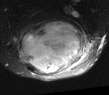
MRI of an extremity soft-tissue mass, one axial slice. Position 25 of 52 along the scan axis. T2-weighted fat-saturated. MR volume resampled by the dataset authors to the PET/CT grid (not the native acquisition matrix). 109 × 95 image matrix, field of view 106 × 93 mm. Male patient. Case-level facts recorded for this patient, not image findings: histological type: synovial sarcoma; site of the primary tumour: left poplietal fossa.
Outlined on this slice (expert contour drawn on MRI and transferred to this co-registered scan by the dataset authors):
- gross tumour volume (mass): box from (x=15, y=17) to (x=87, y=75) px